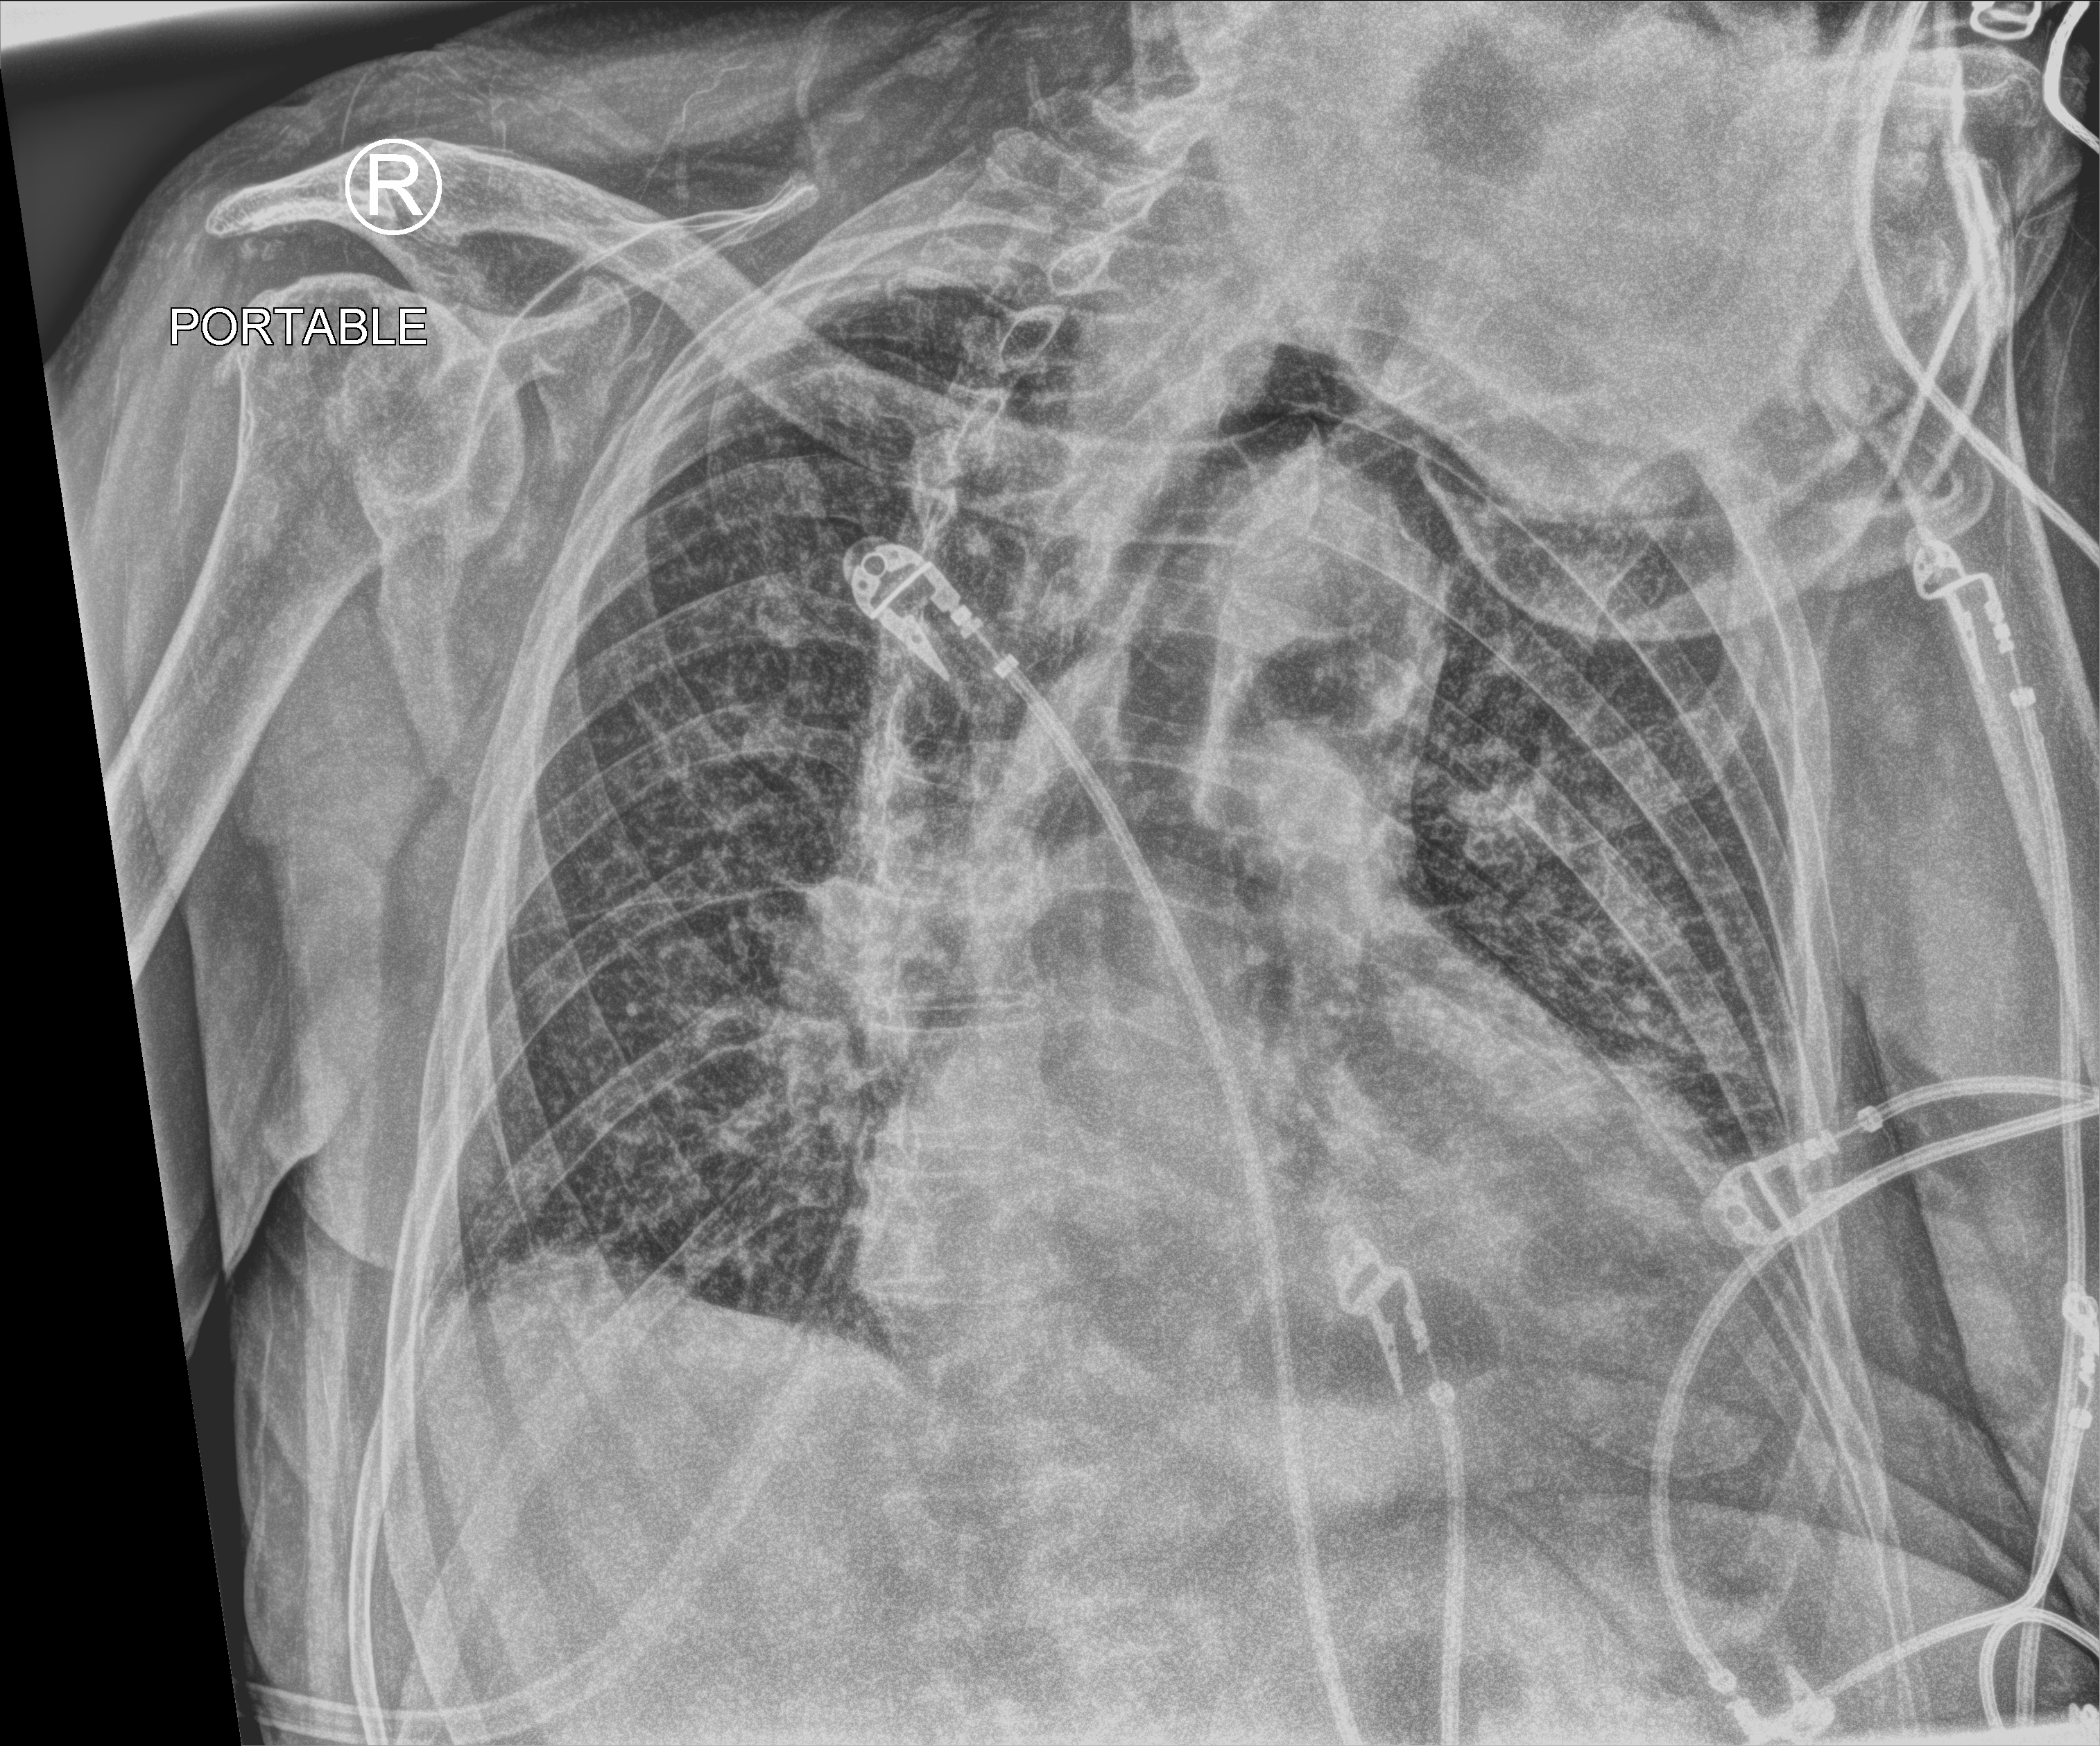
Chest X-ray (portable); anteroposterior (AP) projection. Patient hospitalised with COVID-19; male, aged 75–90 years.
Hospital-stay facts (about this admission, not read from this image; timing relative to this image not recorded): admitted to intensive care during this hospital stay: no; smoking status (admission record): never; mechanically ventilated during this hospital stay: no.